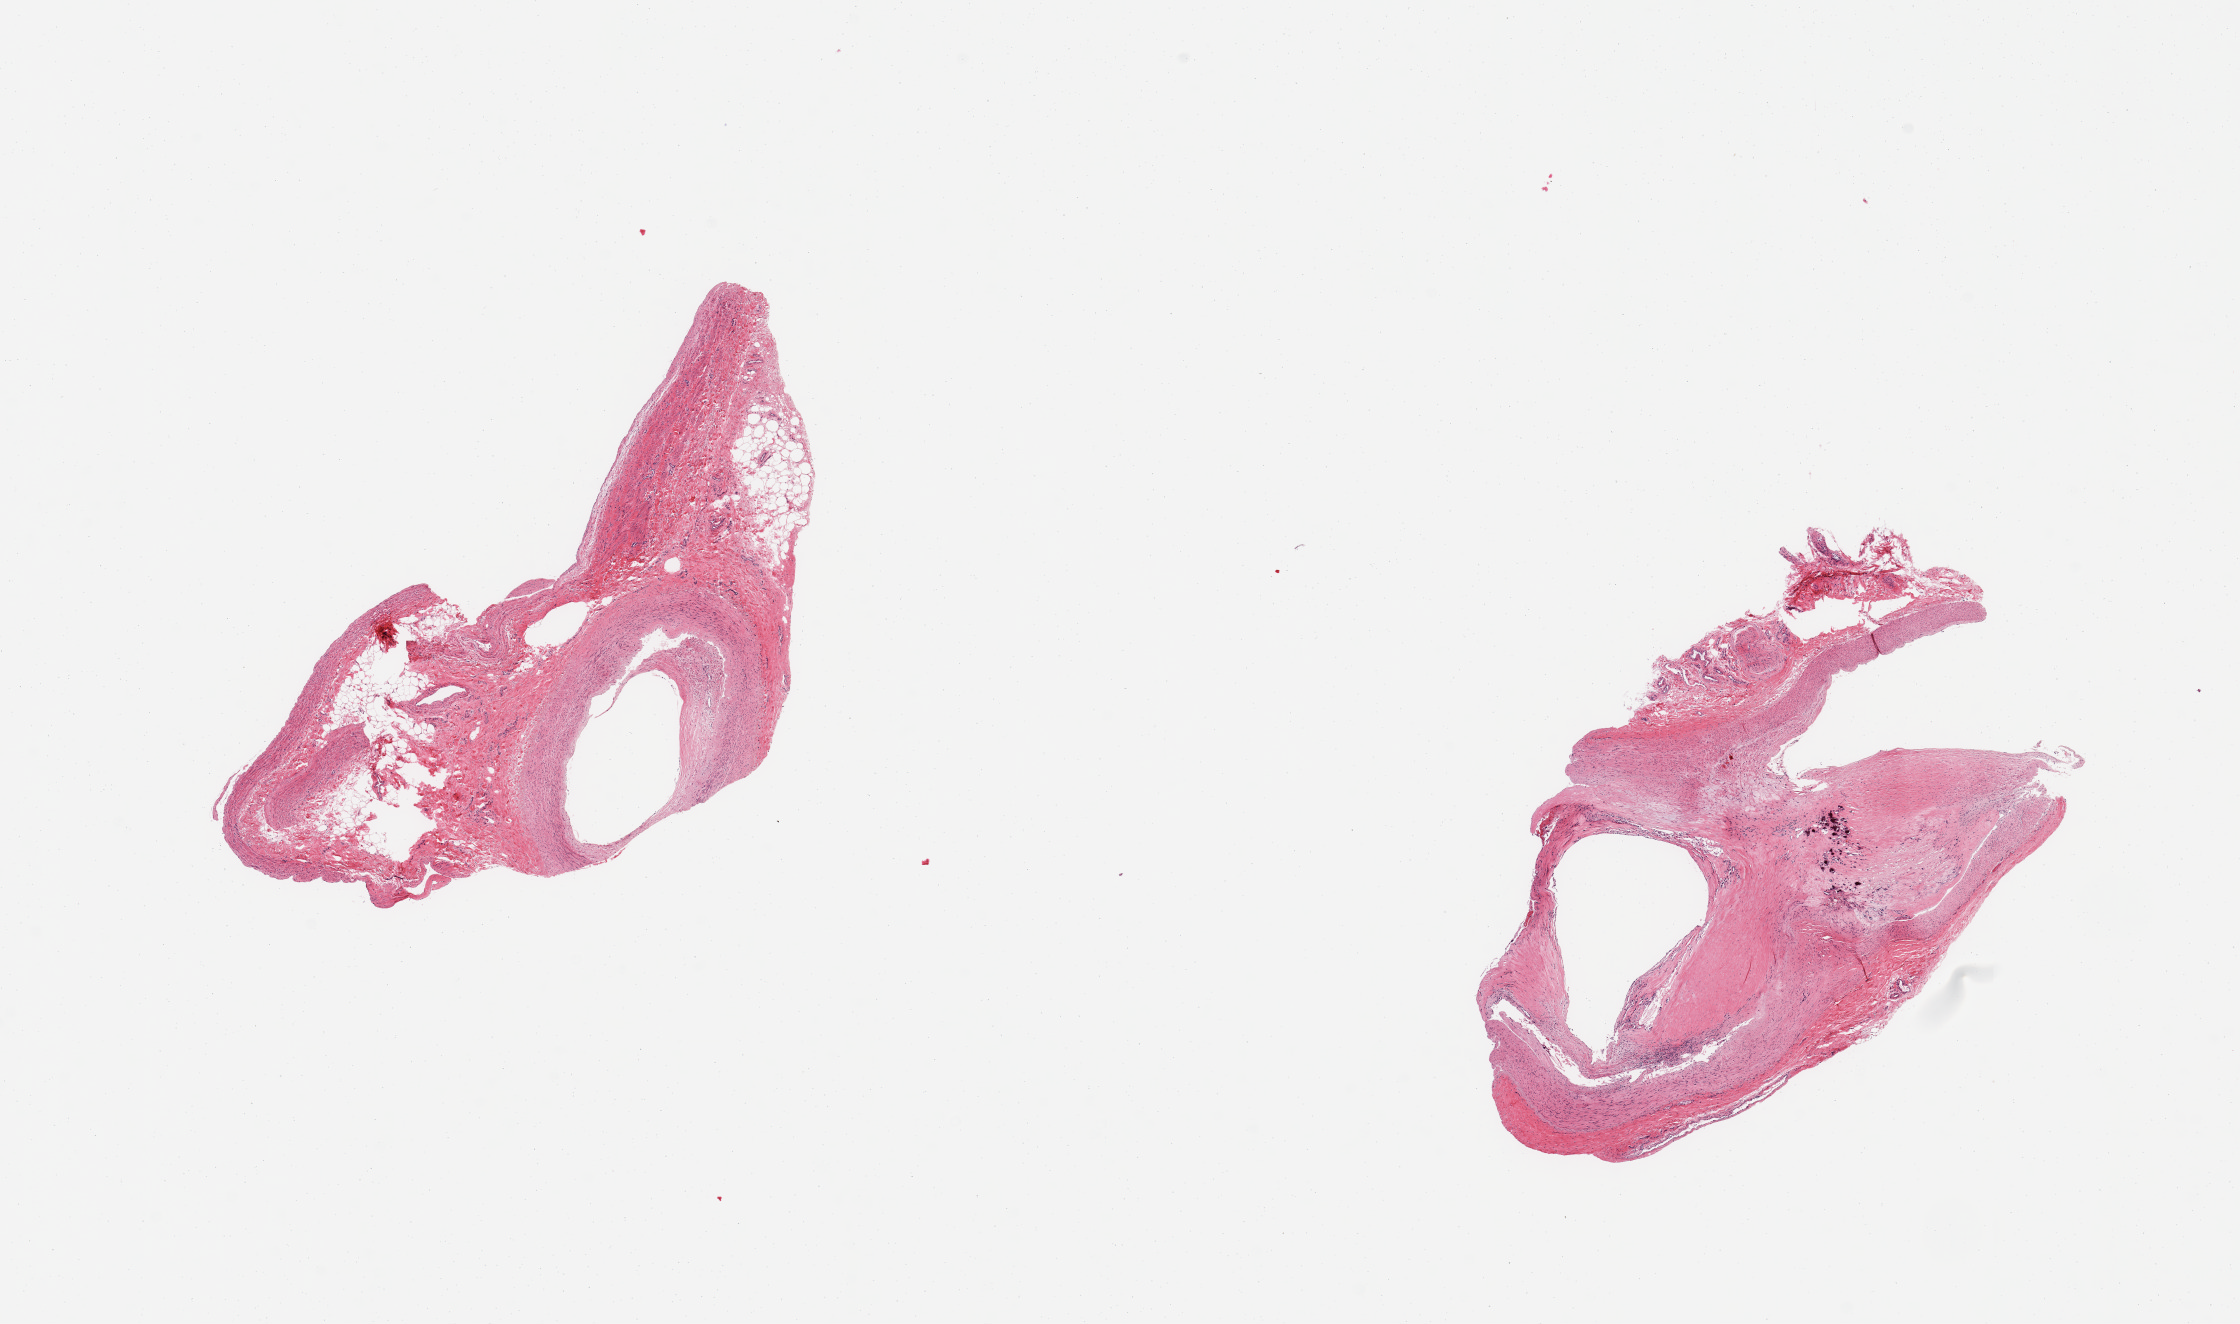
H&E whole-slide image, whole scanned area (about 17.7 x 10.5 mm, from a 20x scan) shown as a low-resolution overview; PAXgene-fixed paraffin-embedded (PFPE) section; sampled site (target tissue): tibial artery; donor tissue sample.
Pathologist's review note for this sample: 2 pieces; large fibrocalcific plaques; abundant external fibrofatty tissue in one.